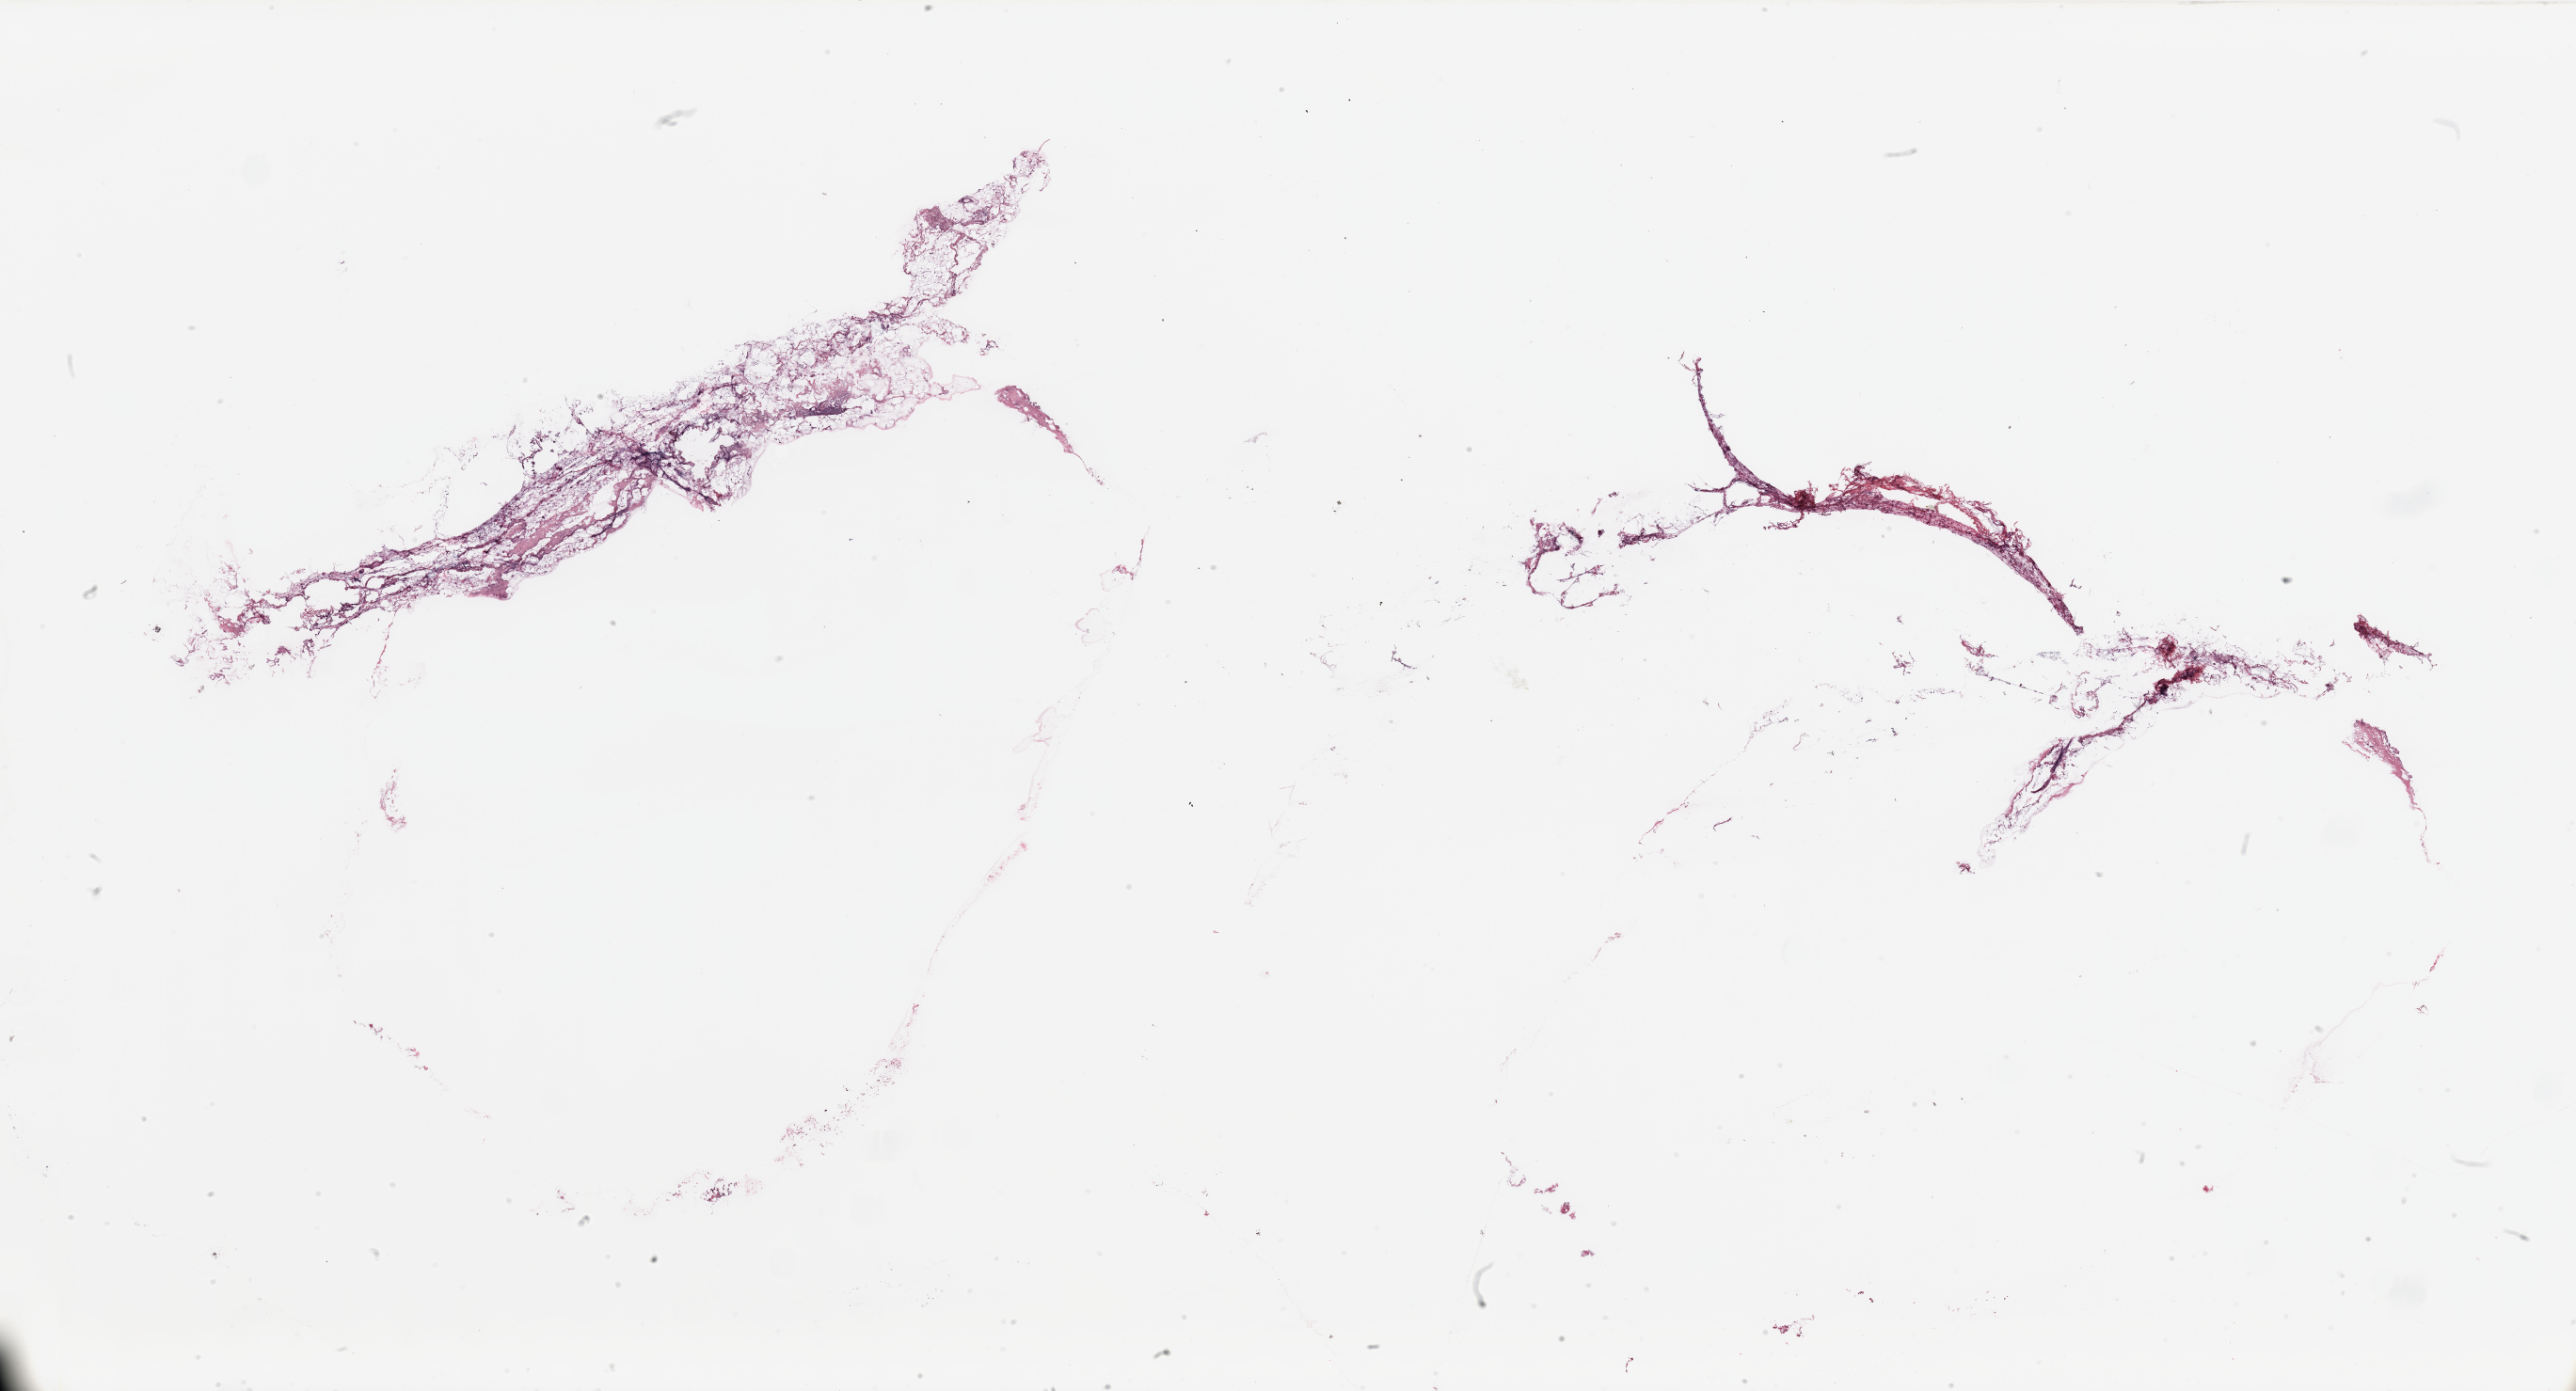
H&E whole-slide image — low-resolution overview of the scanned area, about 43.3 x 23.4 mm; tumour tissue sample, breast. Female, 64 y/o.
* AJCC pathologic stage: IIIA
* diagnosis: Infiltrating duct carcinoma, NOS